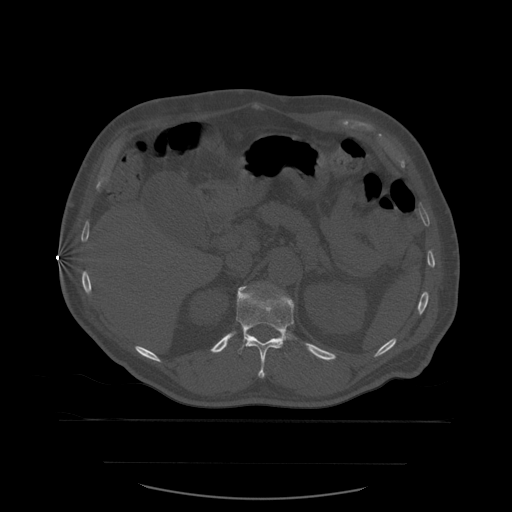
CT including the spine, one axial slice; position 269 of 590 along the scan axis; bone window (W 1800 / L 400 HU); 1.25 mm slice thickness; 512 × 512 image matrix. Patient age 71 years. Case-level facts recorded for this patient, not image findings: primary cancer: lung.
Annotated regions visible in this slice (semi-automatically segmented with operator editing):
- T12 vertebra: box from (x=236, y=286) to (x=295, y=379) px